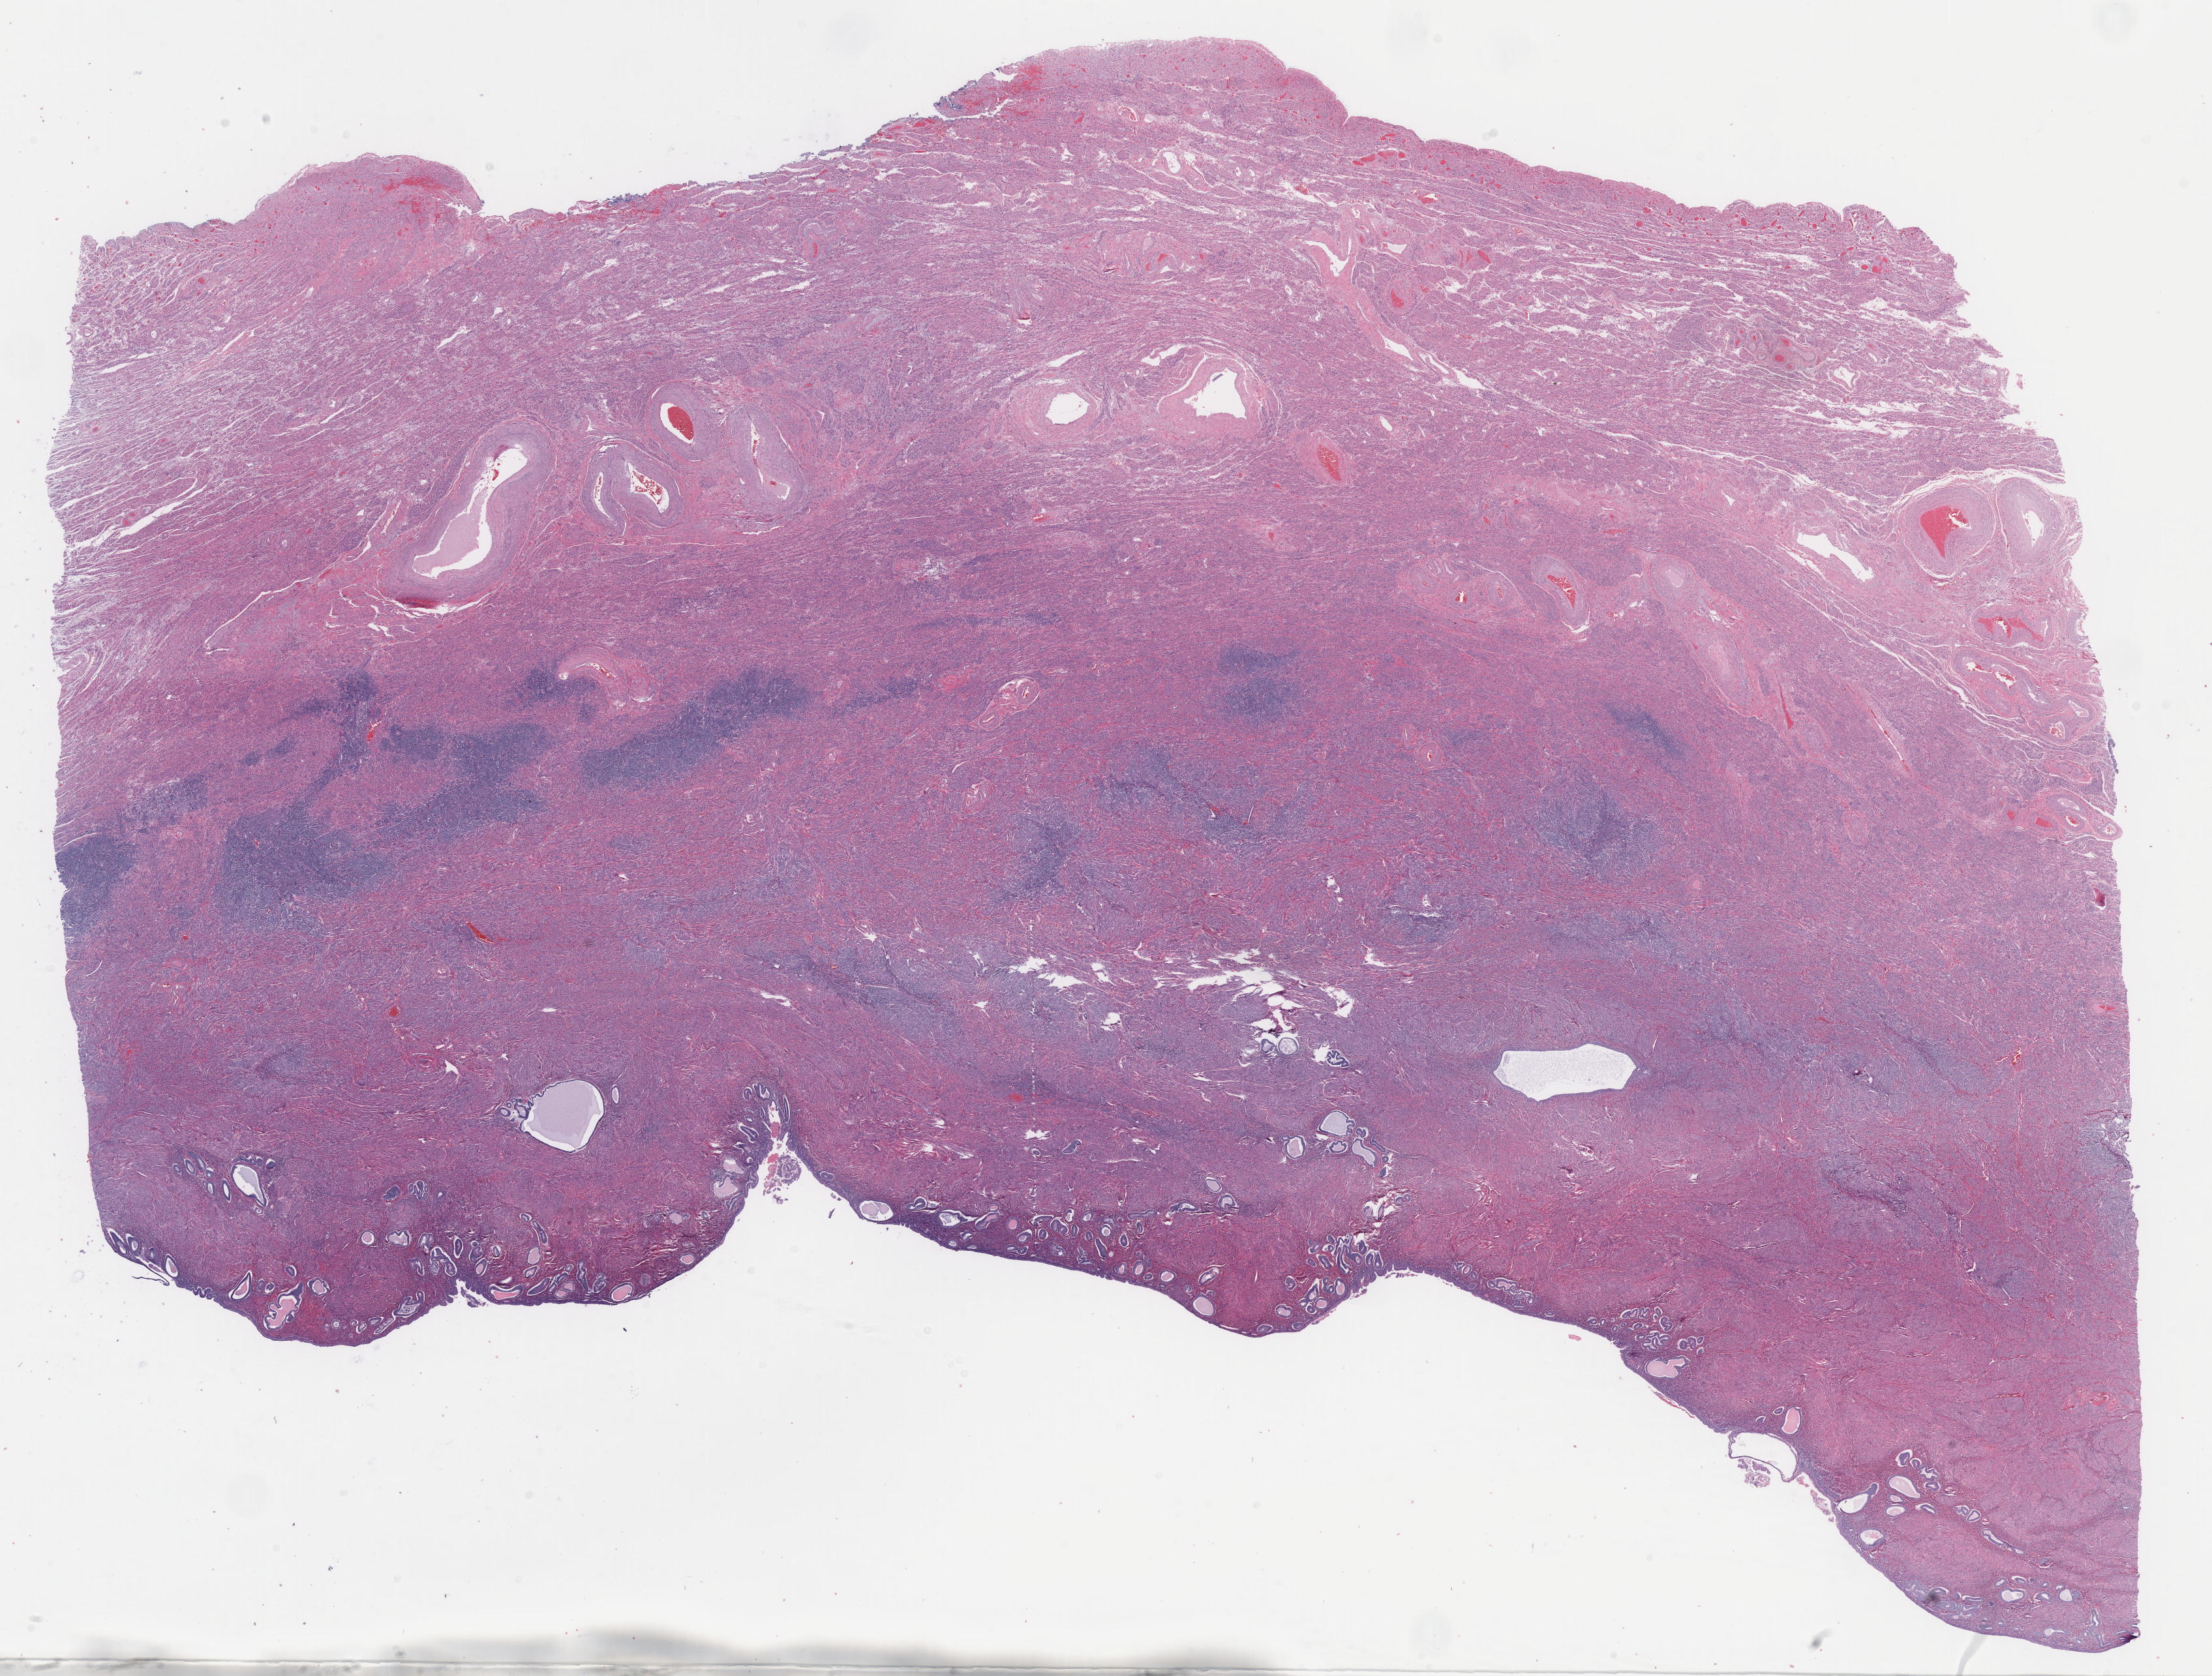
Digitized hematoxylin and eosin (H&E)-stained section, a low-resolution overview of the entire scanned area, about 26.8 x 20.3 mm. Cryosection. Specimen: non-tumor (normal tissue) sample from a patient with serous carcinoma, NOS. Site: isthmus of uterus. Female patient. Composition of this section per pathologist review: tumor cells 0%, tumor nuclei 0%, stromal cells 94%, necrosis 0%, normal cells 6%. Infiltration values recorded for this section: lymphocyte infiltration 1%, monocyte infiltration 1%, neutrophil infiltration 0%.
- this section: non-tumor tissue sample; the patient's diagnosis is given above